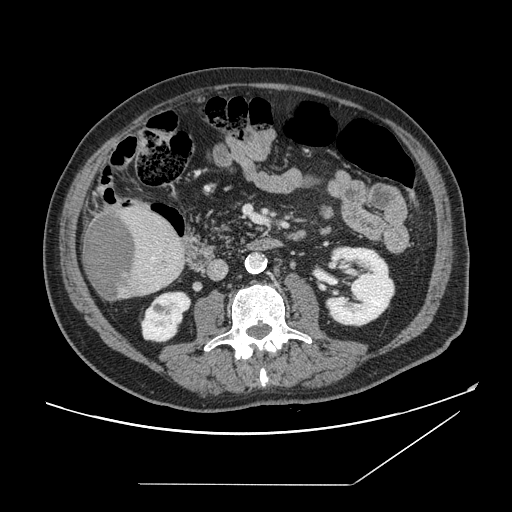
Contrast-enhanced abdominal CT, one axial slice; position 47 of 166 along the scan axis; intravenous contrast given; soft-tissue window (W 400 / L 40 HU); 2.5 mm slice thickness; 512 × 512 image matrix, field of view 416 × 416 mm. Male patient, age 80 years. Case-level facts recorded for this patient, not image findings: diagnosis: colorectal cancer liver metastases, imaged before liver resection; multiple liver metastases: no; largest metastasis: 2.2 cm; disease in both lobes: no.
Structures marked on this image (expert manual segmentation):
- liver: bounding box (x1, y1, x2, y2) in pixels: (83, 204, 186, 301)
- liver metastasis: (84, 210, 137, 300)